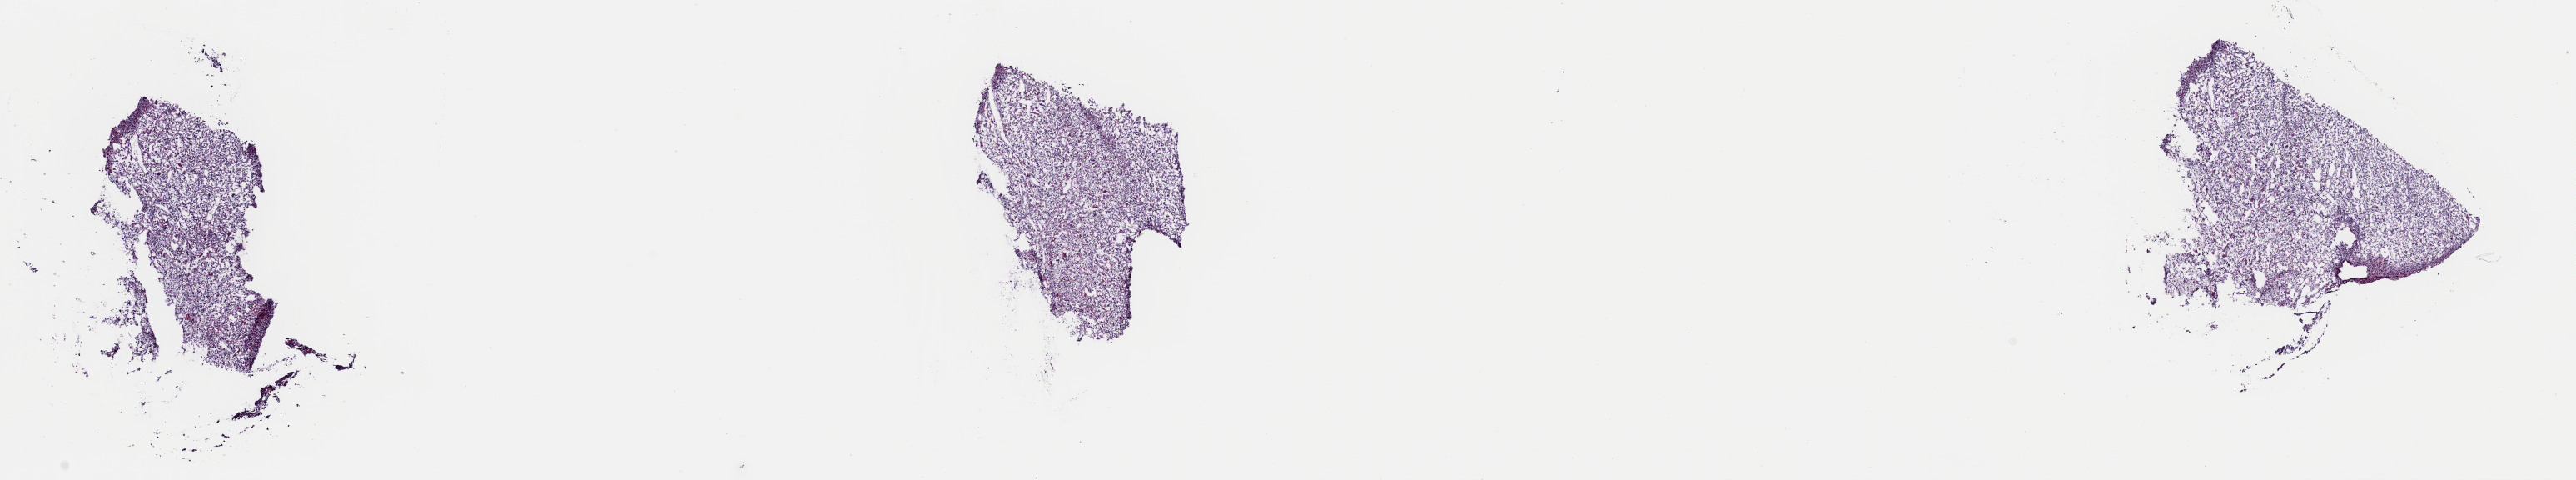
Whole-slide histology image, H&E-stained — whole scanned area (about 24.4 x 4.5 mm, slide scanned at 40x) shown as a low-resolution overview, frozen section, primary tumour sample from the uterus. Female, age 63 years at initial diagnosis.
Diagnosis: Mullerian mixed tumor (endometrium).